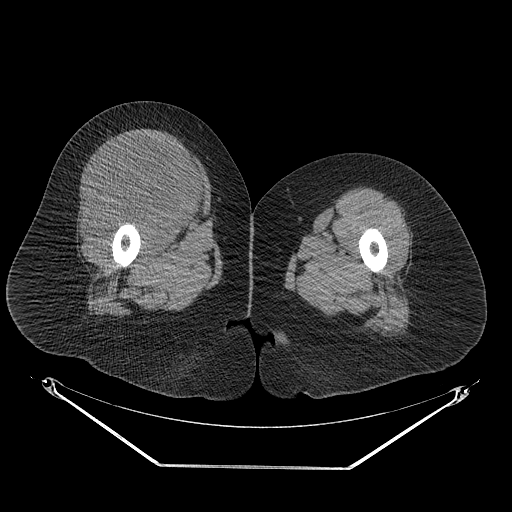
CT of an extremity soft-tissue mass (from a PET/CT study), one axial slice; slice 39 of 267 in the series (ordered by position); soft-tissue window (W 400 / L 40 HU); 512 × 512 image matrix, field of view 500 × 500 mm. Female patient. From the clinical record (not read from this slice): histological type: malignant solitary fibrous tumor; grade: intermediate; site of the primary tumour: right thigh.
Outlined on this slice (expert contour drawn on MRI and transferred to this co-registered scan by the dataset authors):
- gross tumour volume including surrounding oedema: bounding box [x1, y1, x2, y2] px = [82, 135, 209, 232]
- gross tumour volume (mass): [87, 135, 204, 229]